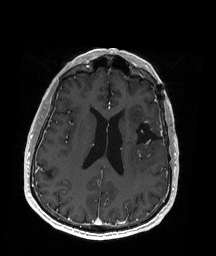
Brain MRI from a brain-tumour surgery series, one axial slice. Slice 79 of 192 in the series (ordered by position). T1-weighted post-contrast. 1 mm slice thickness. 216 × 256 image matrix, field of view 211 × 250 mm. From the clinical record (not read from this slice): histopathology: Oligodendroglioma; WHO grade: 2; IDH mutation: yes.
Annotated regions visible in this slice (manually delineated by an expert):
- previous resection cavity: bounding box (x1, y1, x2, y2) in pixels: (132, 121, 163, 148)